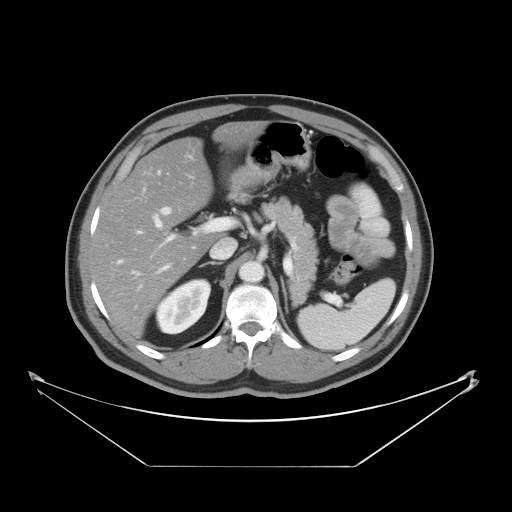
Contrast-enhanced abdominal CT, one axial slice; slice 27 of 46 in the series (ordered by position); reconstruction kernel STANDARD; 120 kVp; intravenous contrast given; soft-tissue window (W 400 / L 40 HU); 5 mm slice thickness; 512 × 512 image matrix, field of view 465 × 465 mm. Male patient, age 57 years. From the clinical record (not read from this slice): diagnosis: colorectal cancer liver metastases, imaged before liver resection; multiple liver metastases: no; largest metastasis: 3.3 cm; chemotherapy before resection: yes.
Structures marked on this image (expert manual segmentation):
- hepatic veins: bounding box [x1, y1, x2, y2] px = [160, 207, 172, 216]
- liver: [94, 139, 221, 336]
- planned liver remnant (the part of the liver to remain after resection): [94, 139, 221, 336]
- portal vein (with intrahepatic branches): [135, 214, 236, 275]